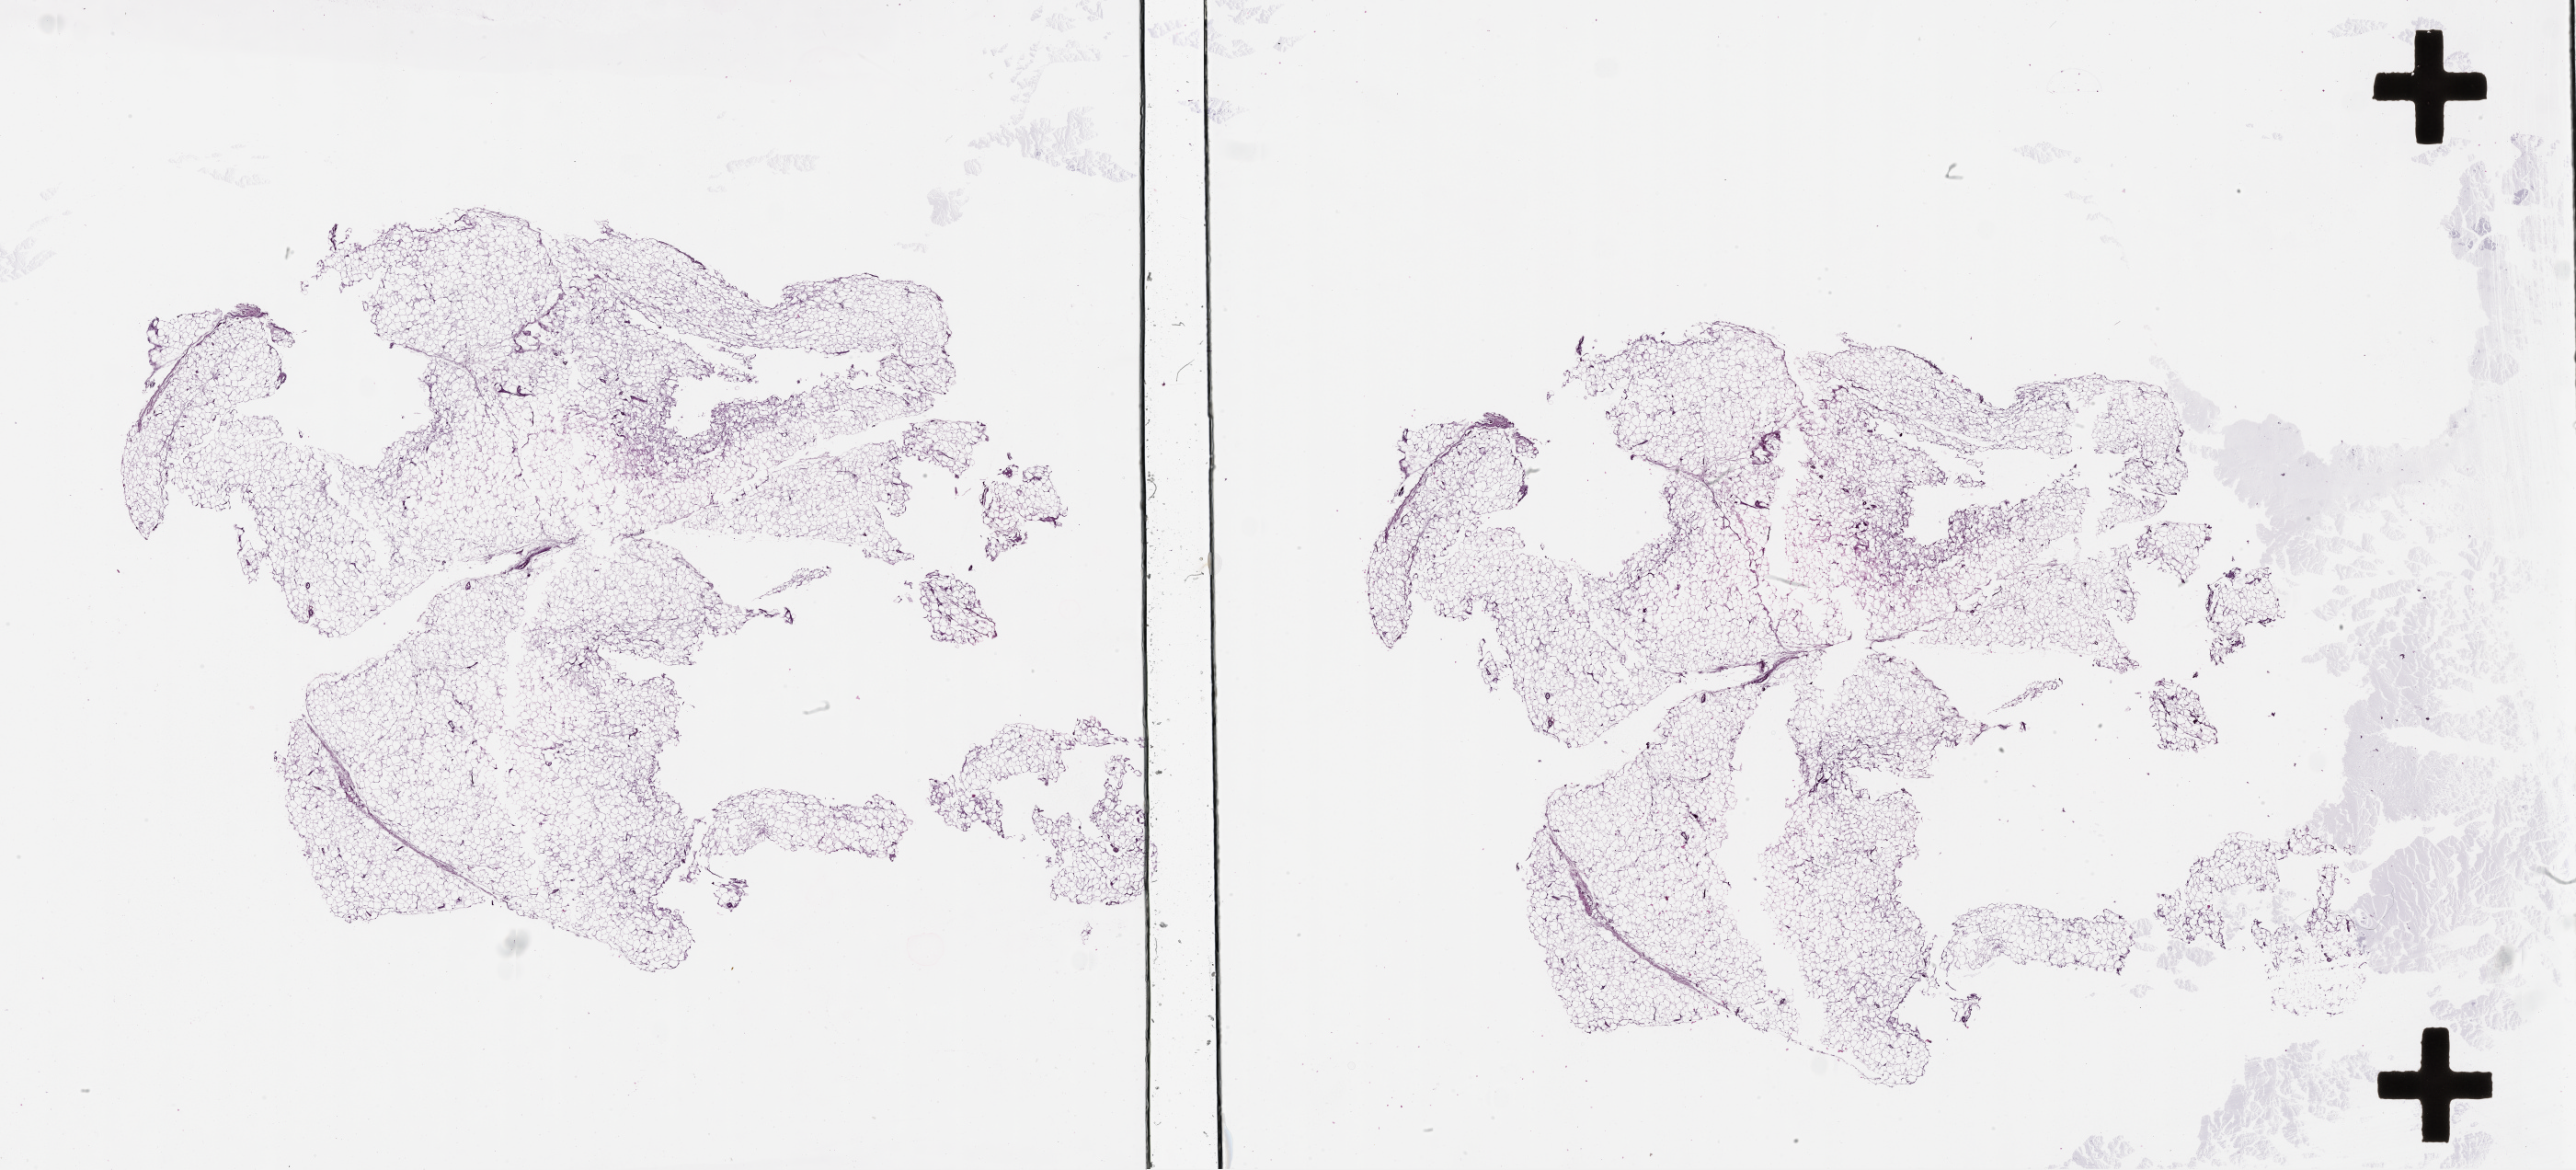
H&E-stained whole-slide image, shown as a low-resolution overview of the whole scanned area (about 45.1 x 20.5 mm, acquisition: 20x scan). Normal (non-tumour) tissue sample. Patient: female, age 78 years.
This section: normal (non-tumour) tissue from the same patient. Patient diagnosis (cohort enrolment): sarcoma (site not recorded at cohort level).